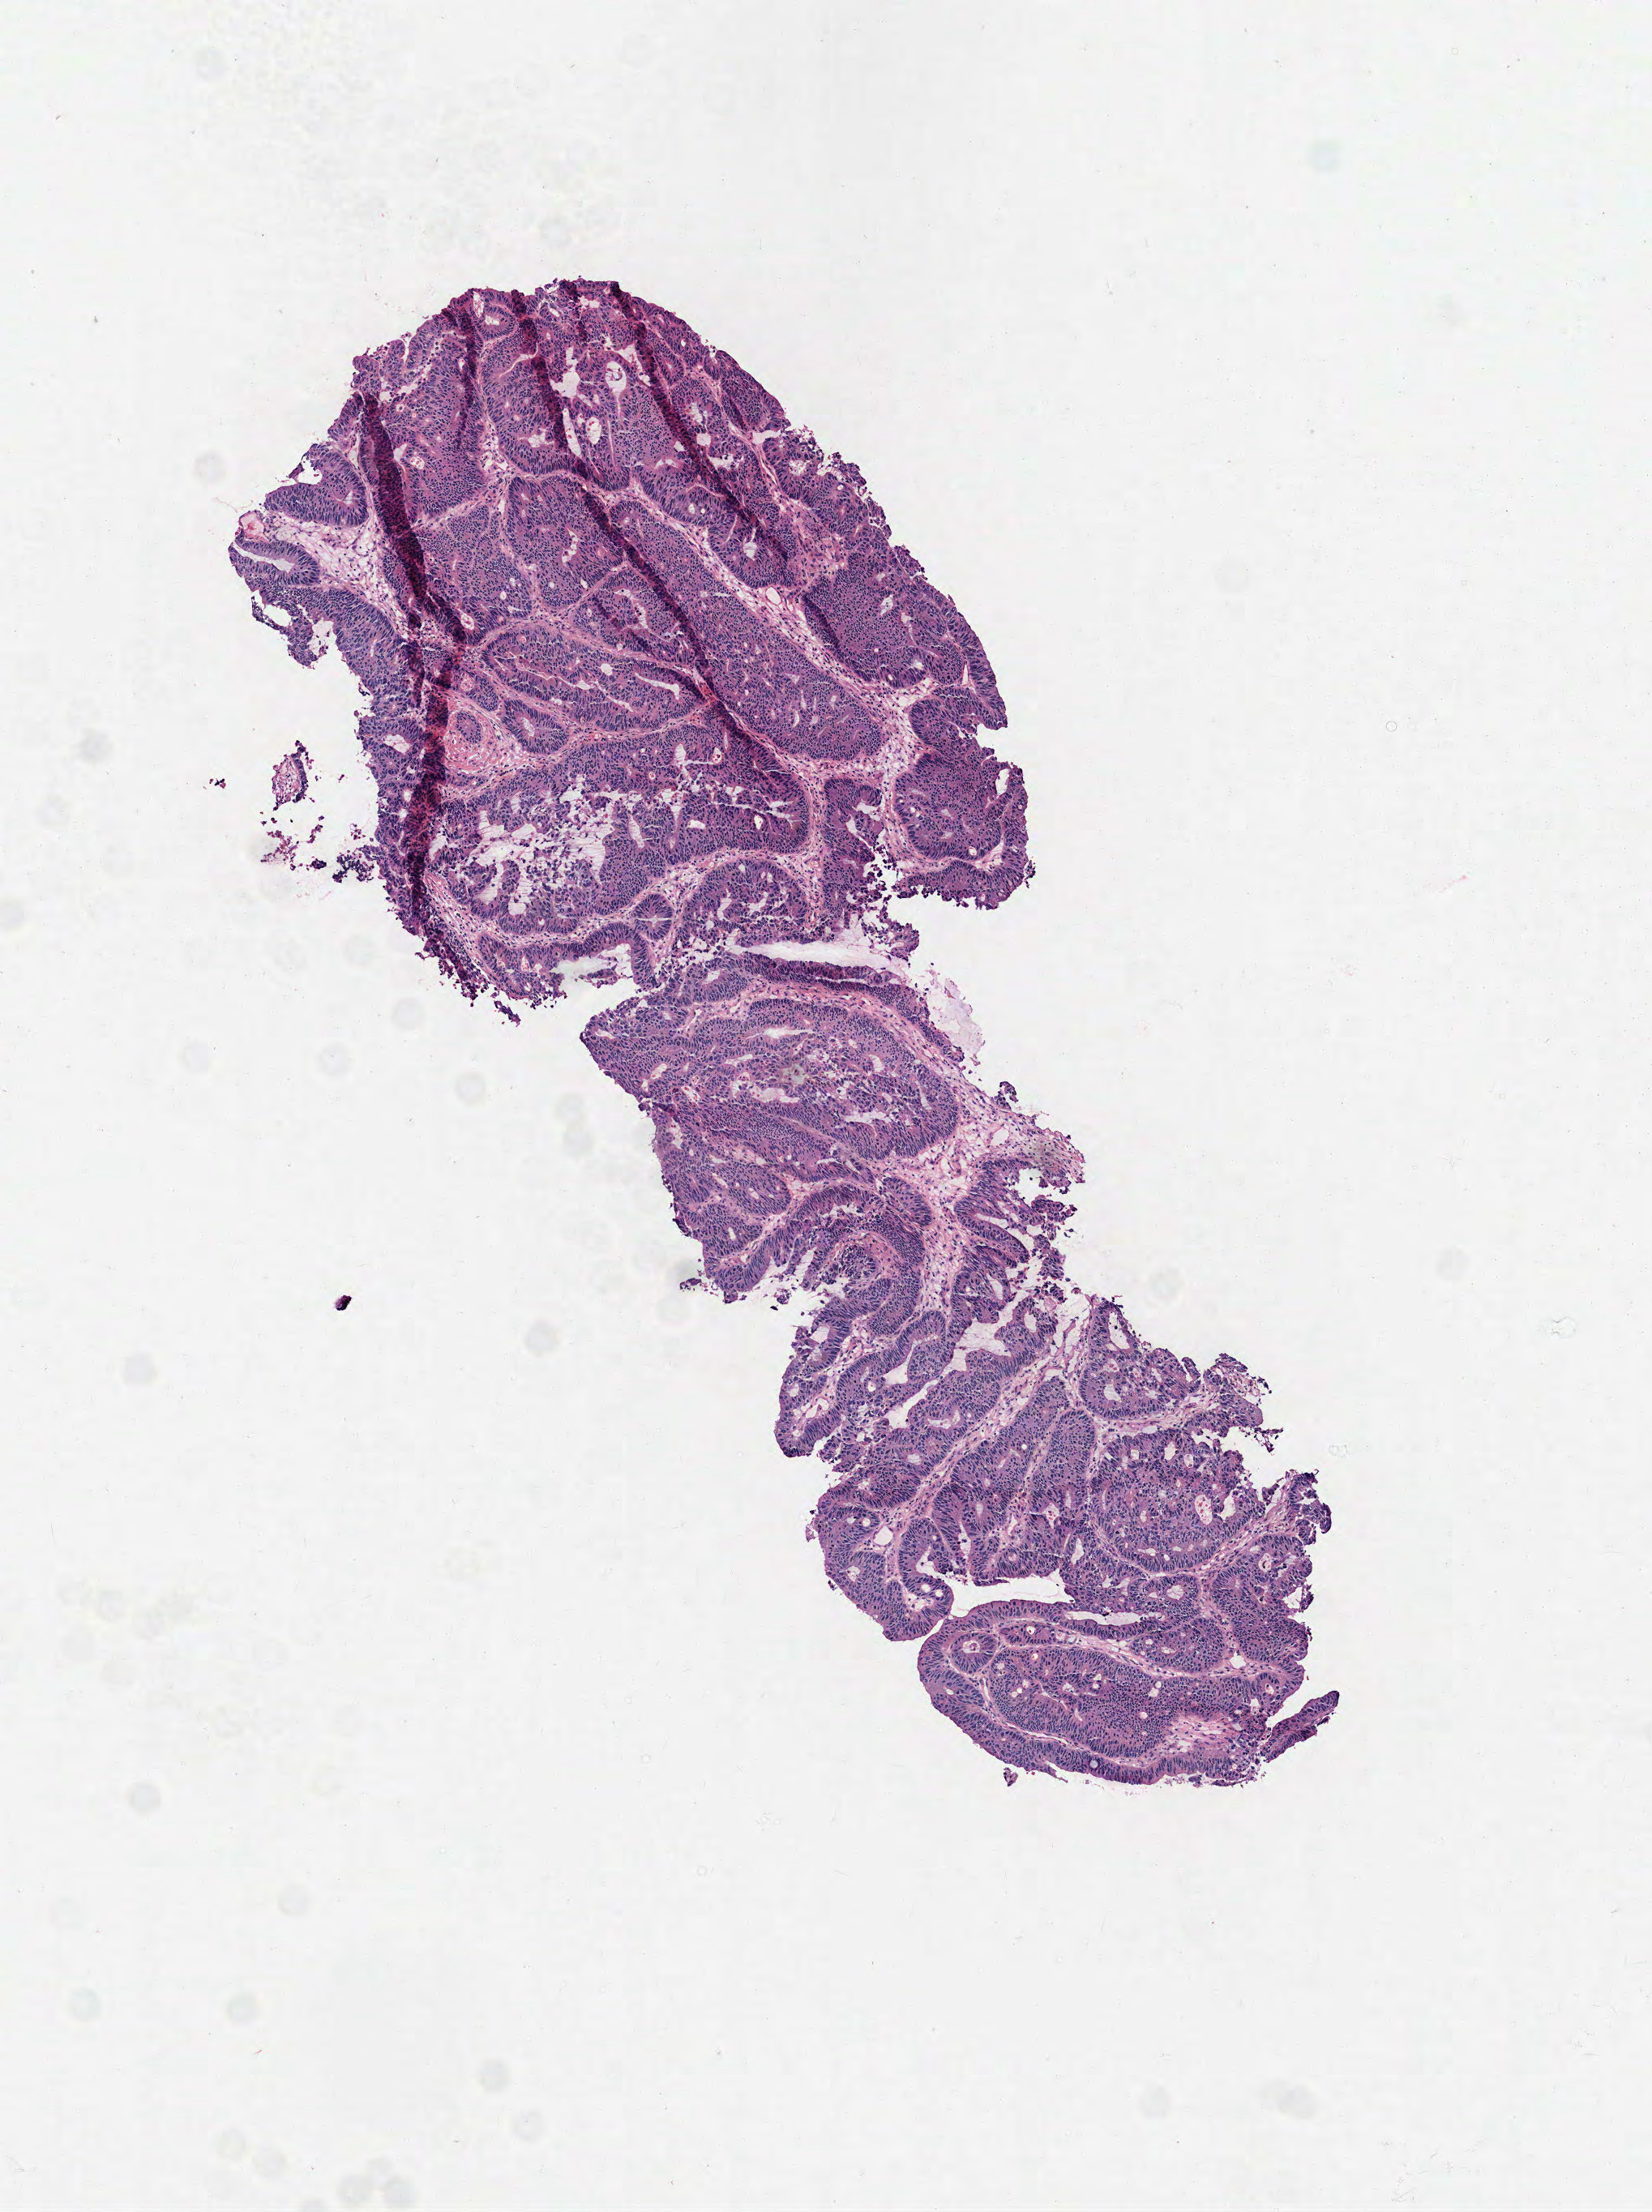
Hematoxylin and eosin (H&E) stained whole-slide image, low-resolution overview of the scanned area, about 4.1 x 5.5 mm (slide scanned at 40x). Frozen section from the top of the tissue portion. Colon, primary tumour sample. Male, age 63 years at initial diagnosis. Composition of this section per pathologist review: tumour cells 94%, tumour nuclei 80%, normal cells 0%, stromal cells 5%, necrosis 1%.
* AJCC pathologic stage: I (6th edition)
* pathologic diagnosis: Adenocarcinoma, NOS